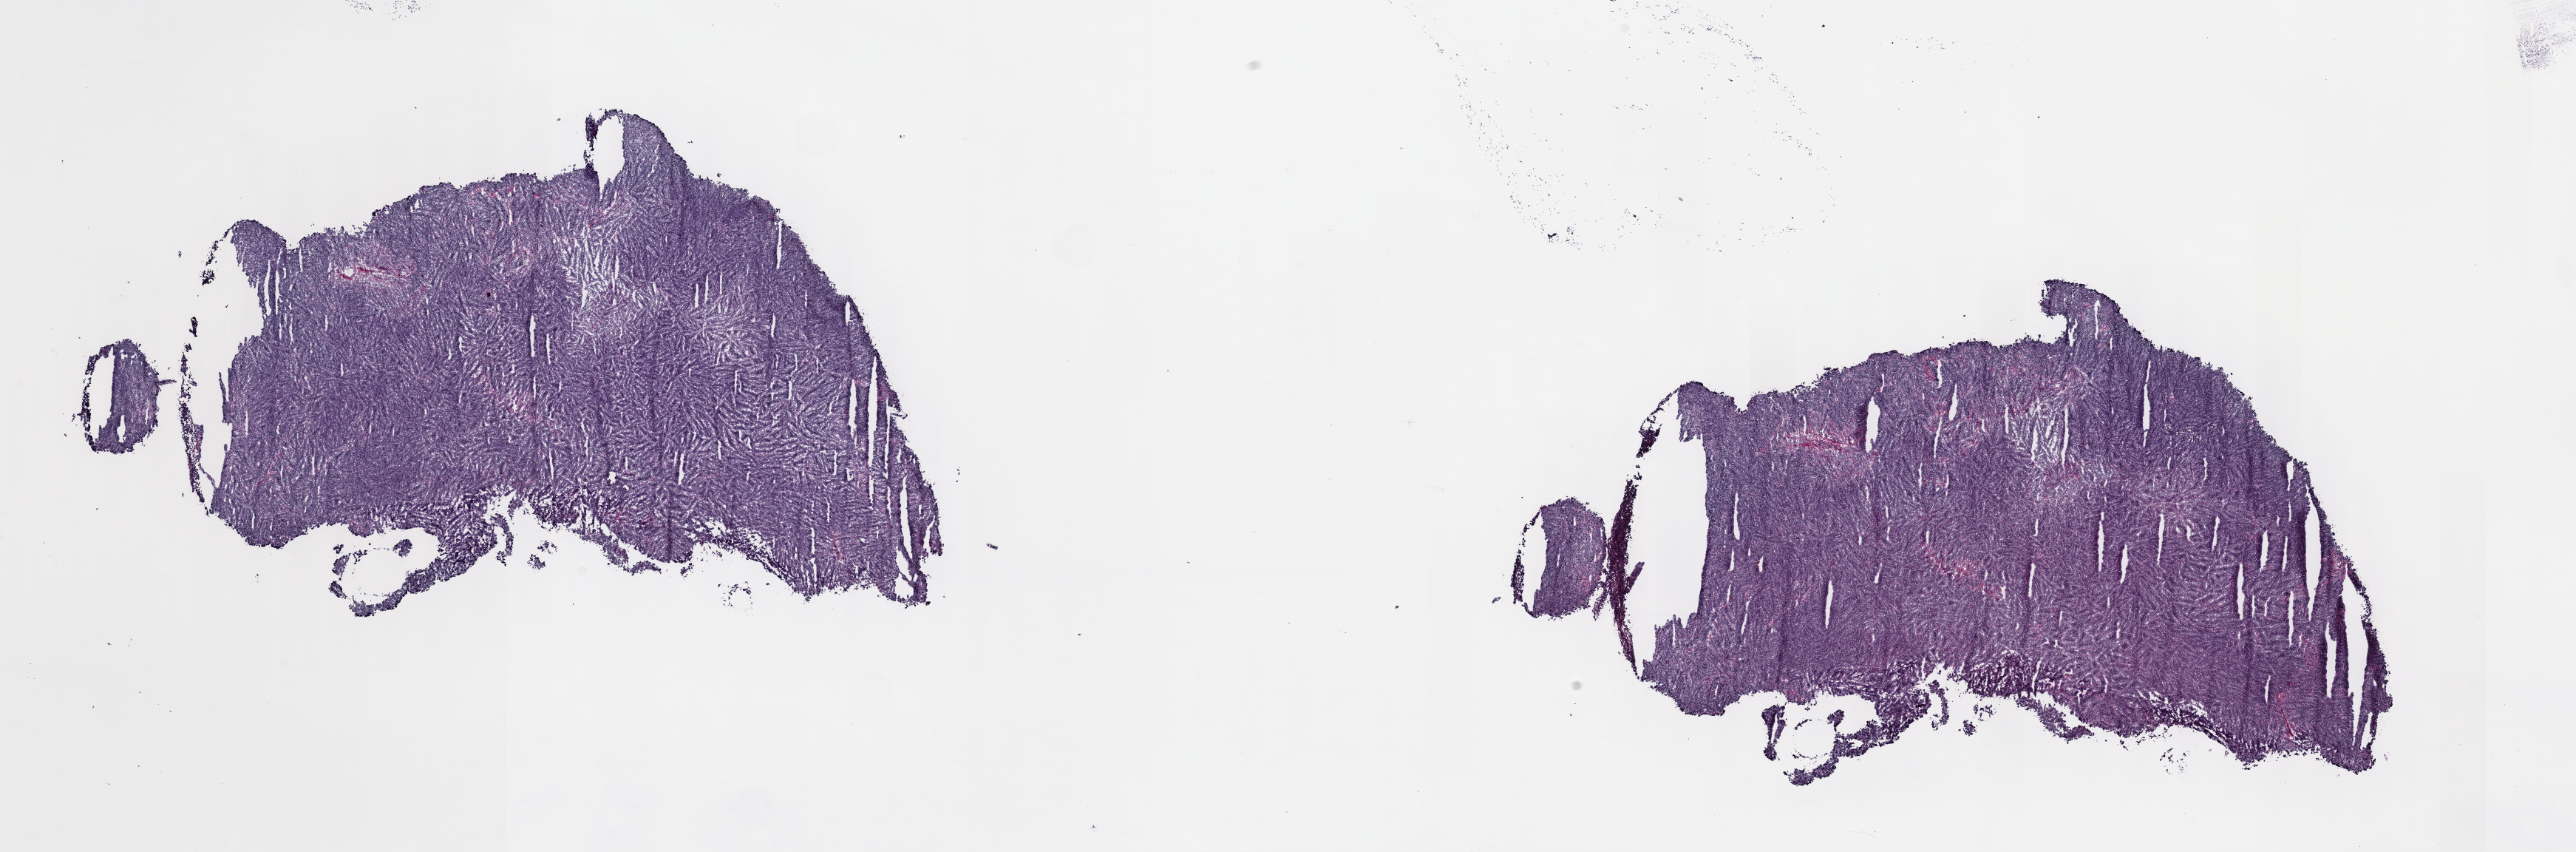
Whole-slide histology image, H&E-stained — a low-resolution overview of the entire scanned area, about 28.2 x 9.3 mm, frozen section from the top of the tissue portion, primary tumour sample from the thymus. Male patient; age at initial diagnosis 44 years. Composition of this section per pathologist review: tumour cells 100%, tumour nuclei 80%, normal cells 0%, stromal cells 0%, necrosis 0%. Inflammatory infiltration, as recorded: lymphocyte infiltration 1%, monocyte infiltration 0%, neutrophil infiltration 0%.
Diagnosis: Thymoma, type B1, malignant (anterior mediastinum).